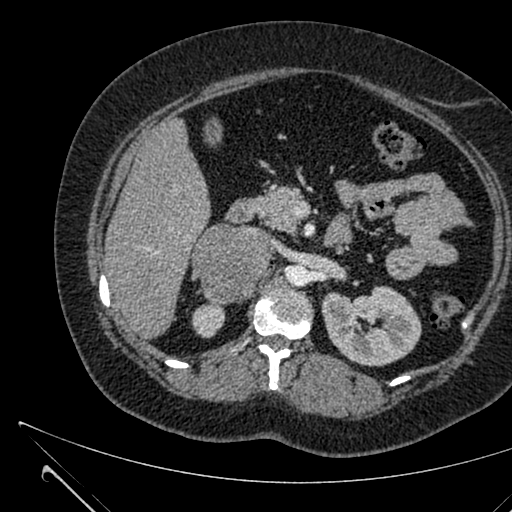
Contrast-enhanced abdominal CT, one axial slice. Slice 385 of 731 in the series (ordered by position). Intravenous contrast given. Soft-tissue window (W 400 / L 40 HU). 1 mm slice thickness. 512 × 512 image matrix, field of view 376 × 376 mm. Female patient, age 36 years. From the clinical record (not read from this slice): diagnosis: adrenocortical carcinoma; tumour side: right adrenal; tumour size at pathology: 10 cm; Ki-67 index: 20 %; stage (as recorded): 4.
Annotated regions visible in this slice (semi-automatically segmented with operator editing):
- mass: bounding box (x1, y1, x2, y2) in pixels: (197, 225, 269, 302)